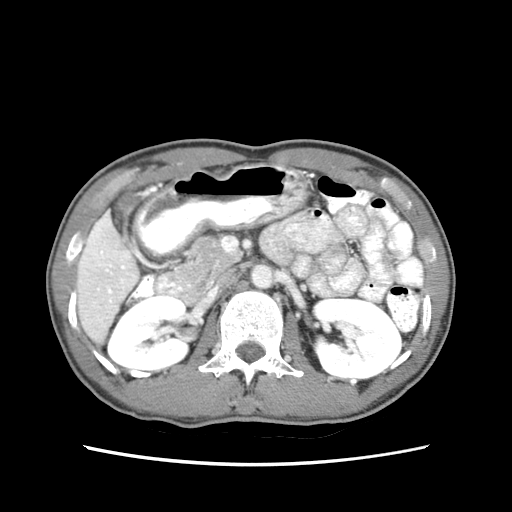
Contrast-enhanced abdominal CT (liver protocol), one axial slice. Slice 24 of 79 in the series (ordered by position). Reconstruction kernel STANDARD. Soft-tissue window (W 400 / L 40 HU). 2.5 mm slice thickness. 512 × 512 image matrix, field of view 320 × 320 mm. From the clinical record (not read from this slice): diagnosis: hepatocellular carcinoma (patient treated with transarterial chemoembolisation; whether this scan precedes or follows treatment is not stated here); TNM stage (as recorded): Stage-IIIB; Child-Pugh class: A; tumour differentiation: moderately differentiated.
Annotated regions visible in this slice (semi-automatically segmented with operator editing):
- liver parenchyma outside the tumour (the mass and vessels are separate outlines, so this box may not span the whole liver): bounding box [x1, y1, x2, y2] px = [76, 211, 138, 342]
- liver vessels: [80, 212, 130, 305]